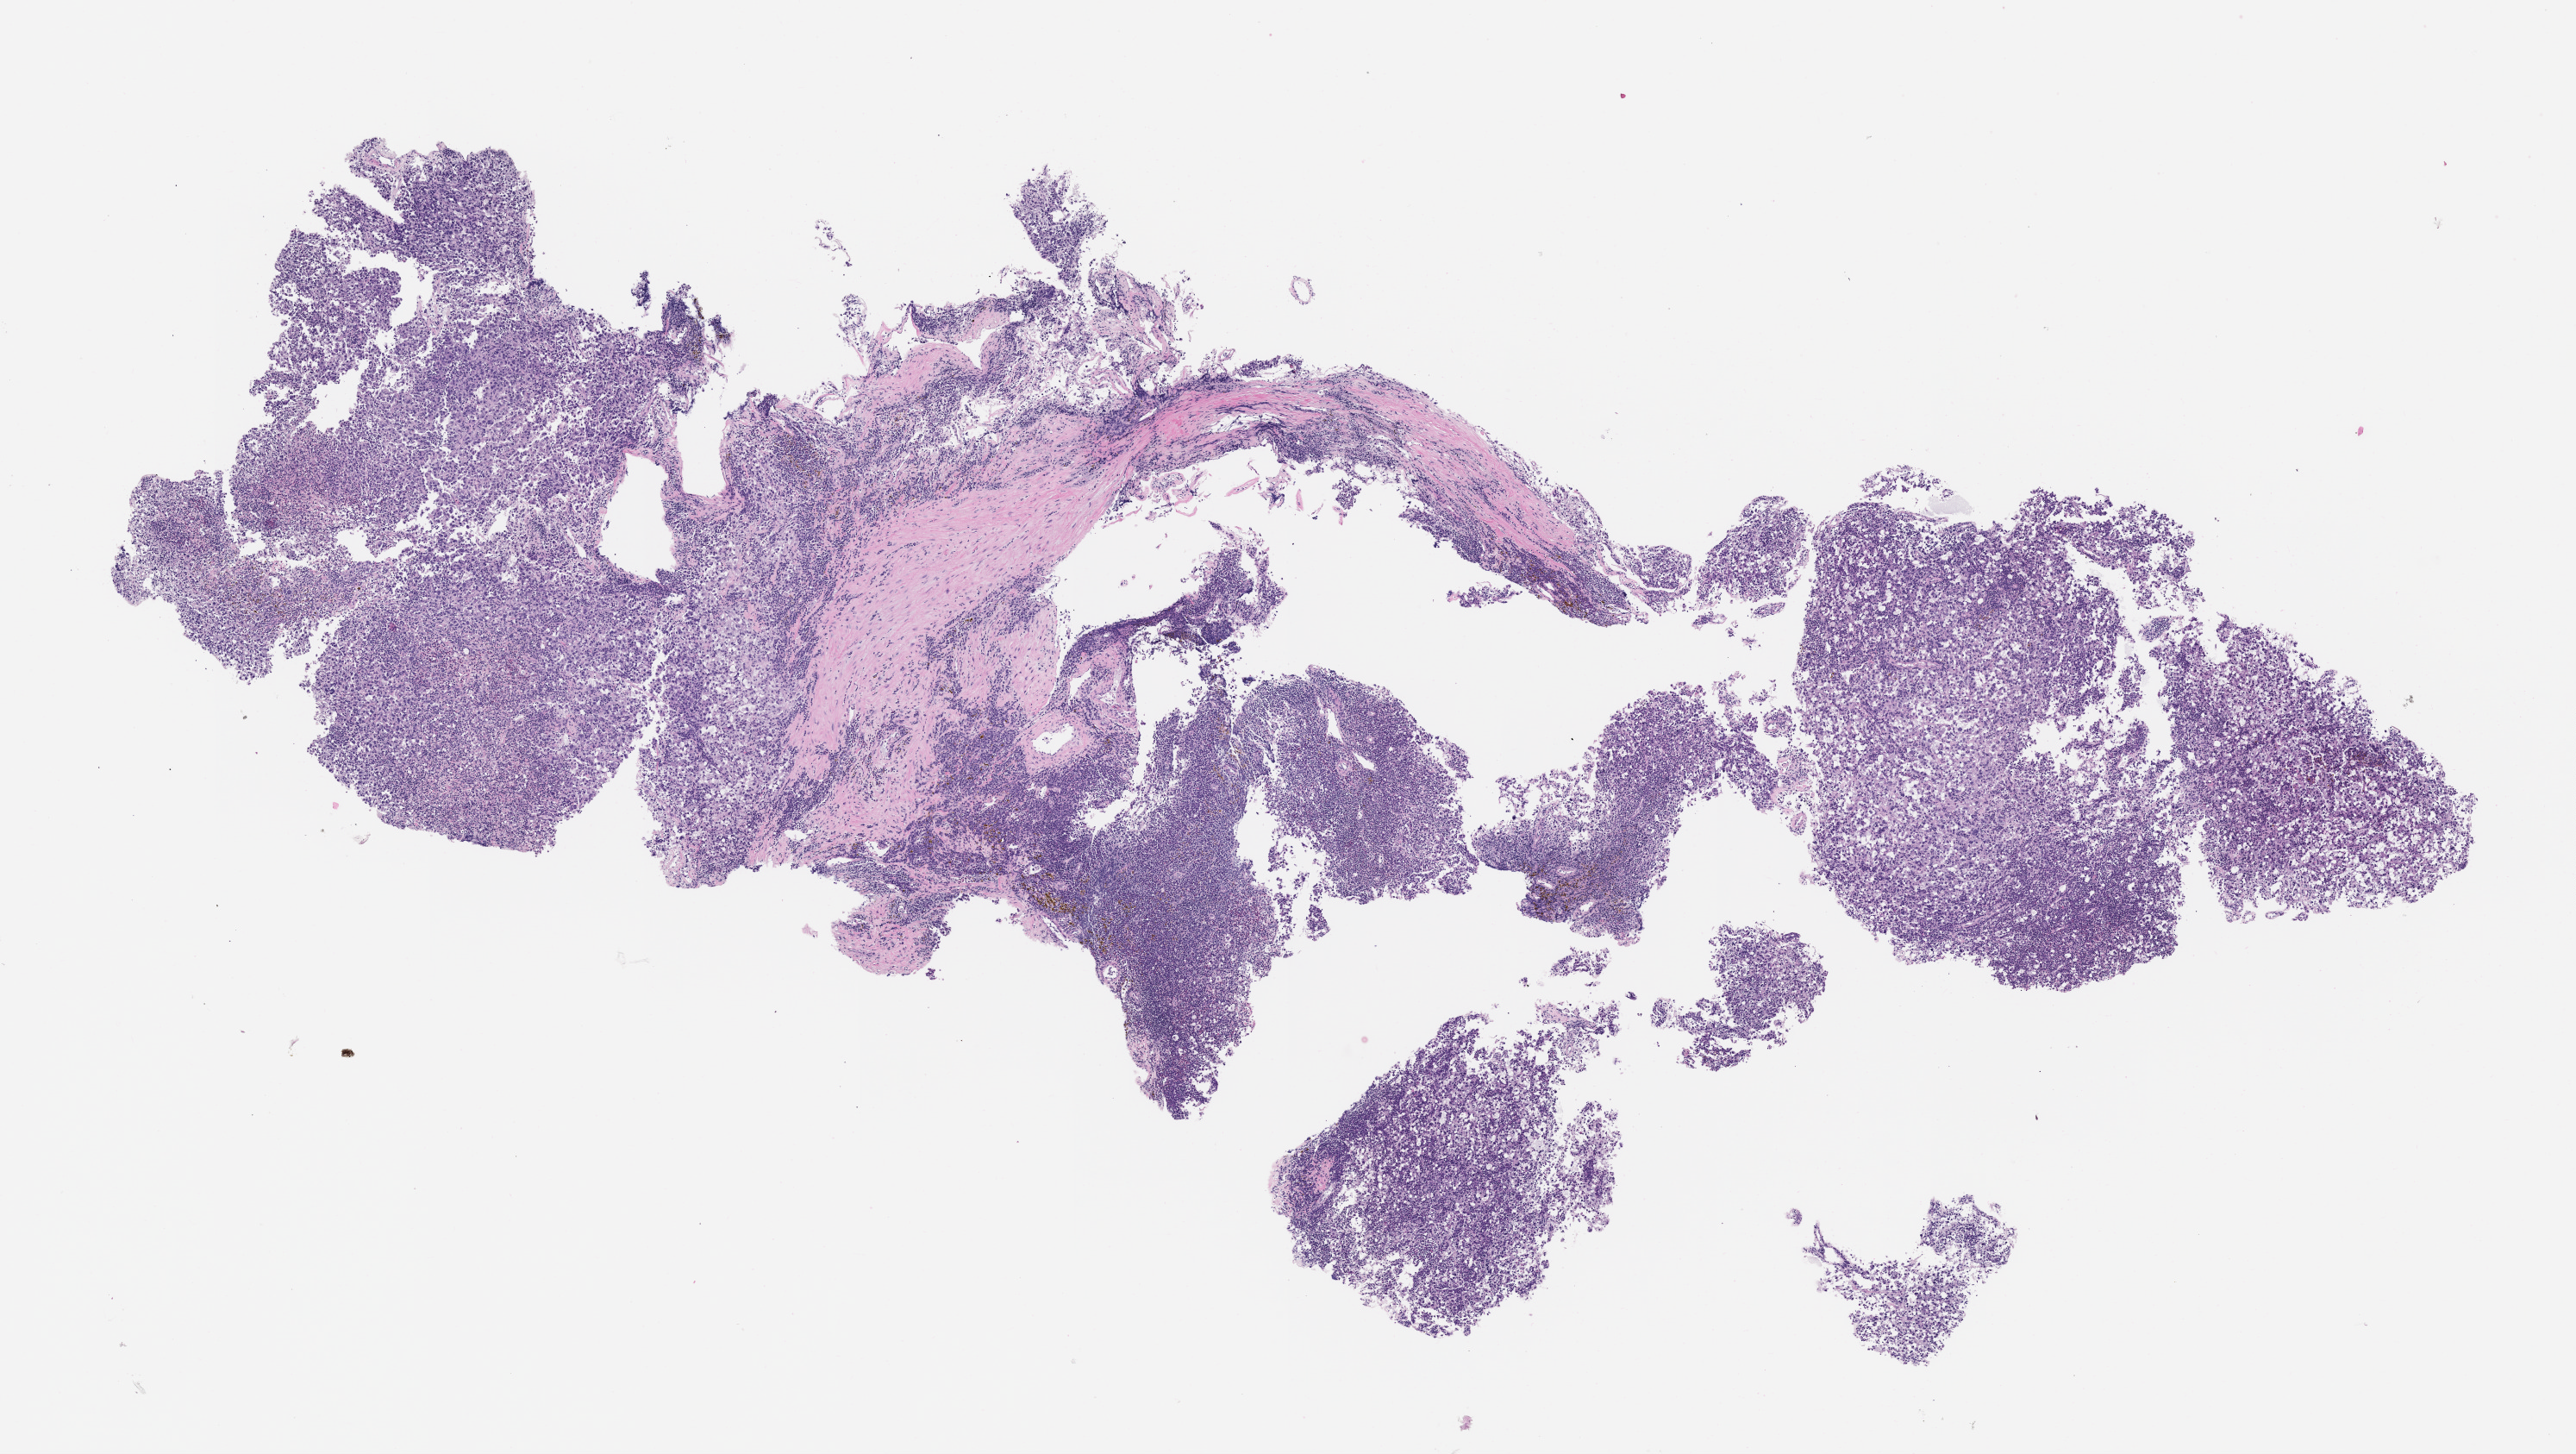
Hematoxylin and eosin (H&E) whole-slide image of the patient's (originator) tumor tissue, whole scanned area (about 12.0 x 6.8 mm) shown as a low-resolution overview. Formalin-fixed, paraffin-embedded (FFPE) tissue. Originating tumor site category: genitourinary tract. Male patient, age 49 years.
• diagnosis: Renal Cell Carcinoma, Not Otherwise Specified